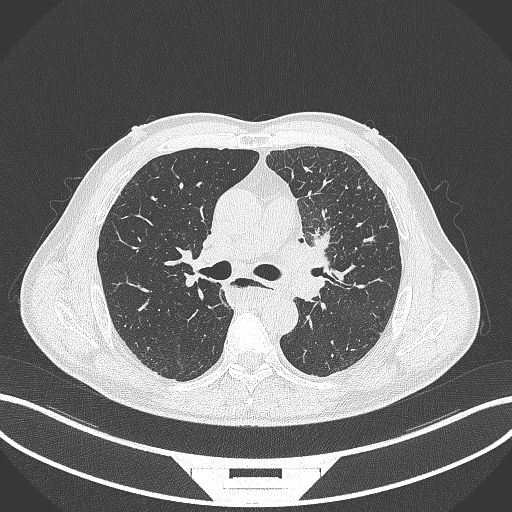
Chest CT, one axial slice. Slice 231 of 411 in the series (ordered by position). Reconstruction kernel B70f. 120 kVp. Lung window (W 1500 / L -600 HU). 1 mm slice thickness. 512 × 512 image matrix, field of view 400 × 400 mm. Patient: male, 57 years. From the clinical record (not read from this slice): clinical TNM (as recorded): T2a N1 M0.
Annotated regions visible in this slice (bounding box drawn by a radiologist):
- lung tumour (recorded histology: squamous cell carcinoma): bounding box (x1, y1, x2, y2) in pixels: (279, 231, 339, 293)